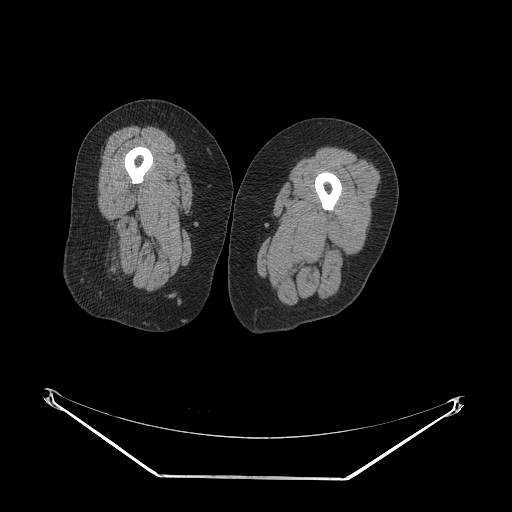
CT of an extremity soft-tissue mass (from a PET/CT study), one axial slice. Slice 20 of 257 in the series (ordered by position). Reconstruction kernel STANDARD. 140 kVp. Soft-tissue window (W 400 / L 40 HU). 512 × 512 image matrix, field of view 500 × 500 mm. Female patient. From the clinical record (not read from this slice): histological type: synovial sarcoma; grade: intermediate; site of the primary tumour: right buttock.
Structures marked on this image (expert contour drawn on MRI and transferred to this co-registered scan by the dataset authors):
- gross tumour volume including surrounding oedema: bounding box (x1, y1, x2, y2) in pixels: (94, 247, 113, 275)